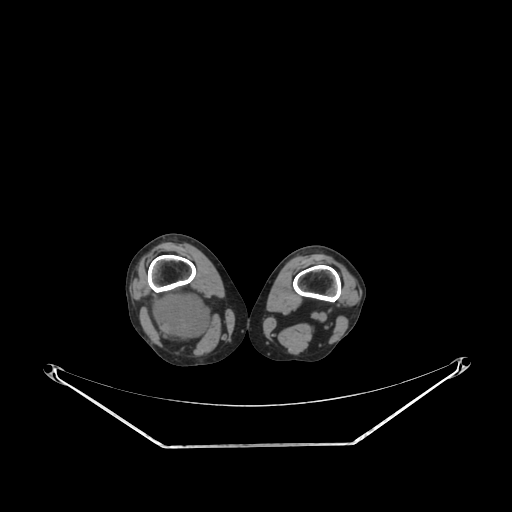
CT of an extremity soft-tissue mass (from a PET/CT study), one axial slice; position 183 of 267 along the scan axis; soft-tissue window (W 400 / L 40 HU); 3.75 mm slice thickness; 512 × 512 image matrix, field of view 500 × 500 mm. Female patient. Case-level facts recorded for this patient, not image findings: histological type: liposarcoma; site of the primary tumour: right thigh.
Outlined on this slice (expert contour drawn on MRI and transferred to this co-registered scan by the dataset authors):
- gross tumour volume (mass): bounding box (x1, y1, x2, y2) in pixels: (148, 288, 213, 344)